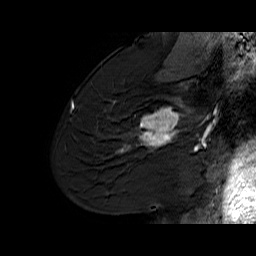
Breast MRI (dynamic contrast-enhanced), one sagittal slice. Slice 40 of 60 in the series (ordered by position). Dynamic contrast-enhanced series, time point 2 of 6 at this slice position (early post-contrast). 1.5 T. TE 6.1 ms, TR 32.9 ms. 4 mm slice thickness. 256 × 256 image matrix, field of view 220 × 220 mm. Female patient. Case-level facts recorded for this patient, not image findings: setting: breast cancer imaged before/during neoadjuvant chemotherapy; receptor status: HER2-positive.
Annotated regions visible in this slice (semi-automatic segmentation, software-assisted and operator-edited):
- analysis volume of interest (the breast-tissue region the enhancement analysis was run in; not a lesion): bounding box [x1, y1, x2, y2] px = [127, 95, 194, 165]
- tumour enhancement mask (voxels above the 100 % enhancement threshold inside the analysis volume of interest): [127, 97, 194, 151]